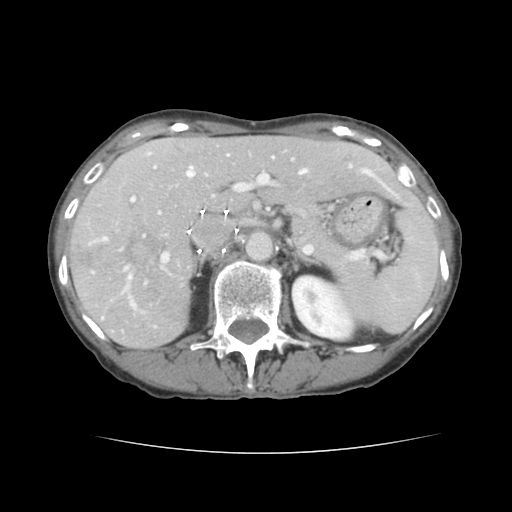
Contrast-enhanced abdominal CT, one axial slice; slice 87 of 136 in the series (ordered by position); 120 kVp; intravenous contrast given; soft-tissue window (W 400 / L 40 HU); 2.5 mm slice thickness; 512 × 512 image matrix, field of view 319 × 319 mm. Female patient, age 77 years. From the clinical record (not read from this slice): diagnosis: colorectal cancer liver metastases, imaged before liver resection; multiple liver metastases: yes; largest metastasis: 3 cm; disease in both lobes: no.
Structures marked on this image (outlined manually by an expert reader):
- hepatic veins: bounding box <187,155,389,190> (left, top, right, bottom; pixels)
- liver: <69,136,420,348>
- planned liver remnant (the part of the liver to remain after resection): <153,136,418,212>
- portal vein (with intrahepatic branches): <103,158,381,309>
- liver metastasis: <75,227,167,267>